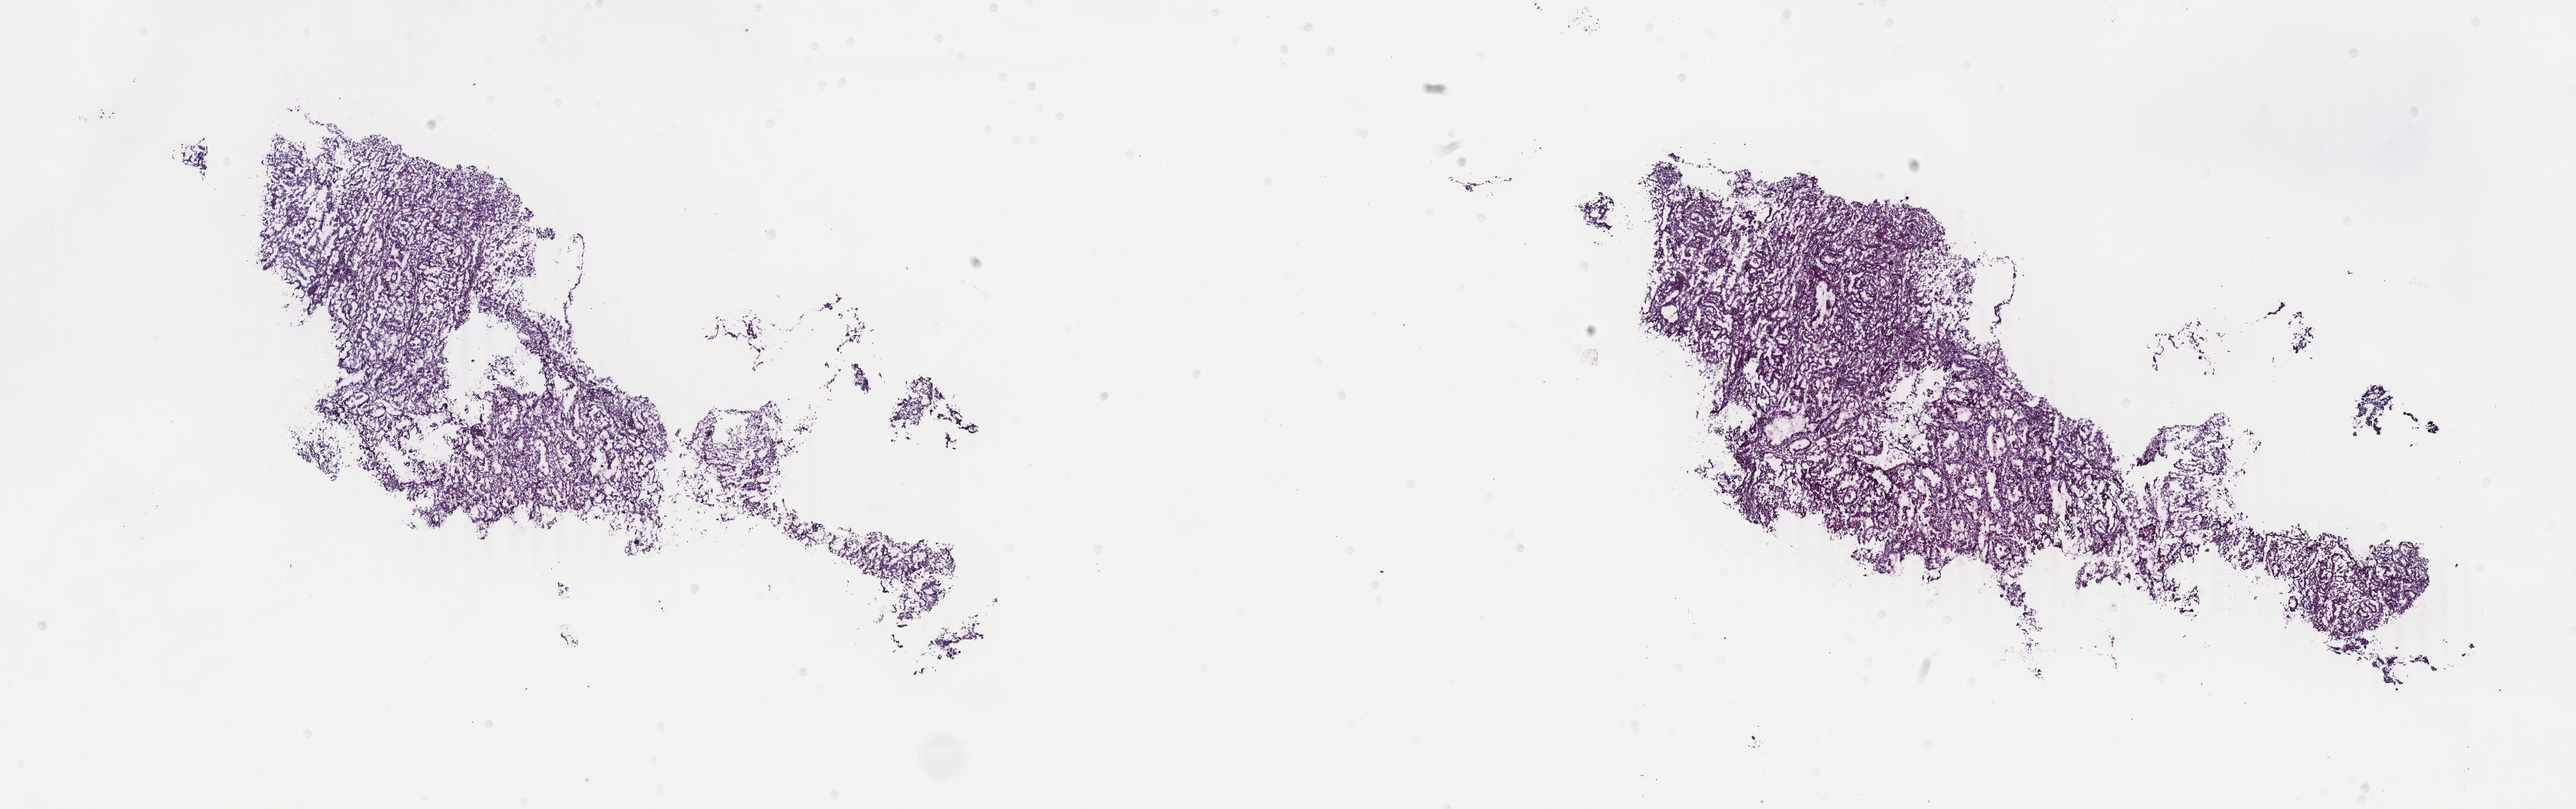
Digitized H&E-stained tissue section (whole slide) — whole scanned area (about 26.7 x 8.4 mm, slide scanned at 40x) shown as a low-resolution overview; frozen section from the bottom of the tissue portion; sample: primary tumour, uterus. Patient: female, age at initial diagnosis 54 years. Histologic grade: G1 (well differentiated). Composition of this section per pathologist review: tumour cells 100%, tumour nuclei 85%, normal cells 0%, stromal cells 0%, necrosis 0%. Inflammatory infiltration, as recorded: lymphocyte infiltration 0%, monocyte infiltration 0%, neutrophil infiltration 0%.
• FIGO stage: IA
• diagnosis: Endometrioid adenocarcinoma, NOS
• lymph nodes positive (case pathology): 0 of 28 examined